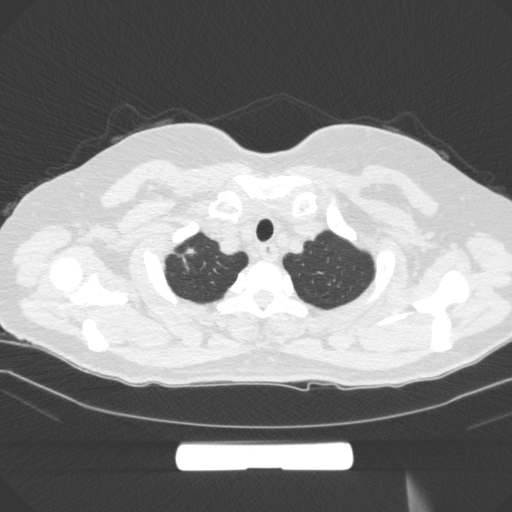
Chest CT, one axial slice. Position 266 of 295 along the scan axis. 120 kVp. Lung window (W 1500 / L -600 HU). 1 mm slice thickness. 512 × 512 image matrix. Female patient, age 58 years. From the clinical record (not read from this slice): clinical TNM (as recorded): T1b N0 M0.
Outlined on this slice (bounding box drawn by a radiologist):
- lung tumour (recorded histology: adenocarcinoma): bounding box <178,238,204,279> (left, top, right, bottom; pixels)